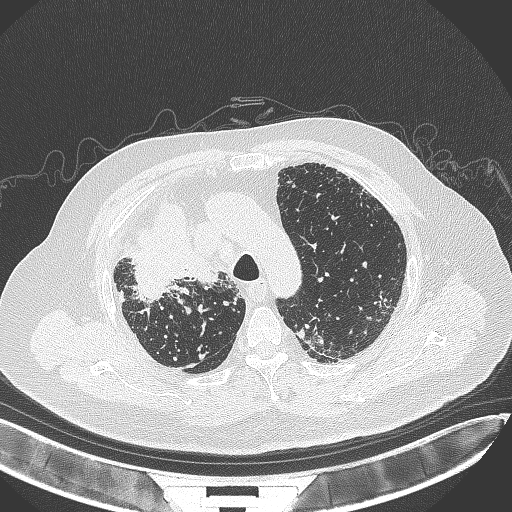
Chest CT, one axial slice. Position 269 of 384 along the scan axis. Lung window (W 1500 / L -600 HU). 1 mm slice thickness. 512 × 512 image matrix, field of view 400 × 400 mm. Male patient, age 69 years. From the clinical record (not read from this slice): clinical TNM (as recorded): T4 N3 M1.
Annotated regions visible in this slice (rectangle marked by the reading radiologist):
- lung tumour (recorded histology: adenocarcinoma): bounding box (x1, y1, x2, y2) in pixels: (123, 201, 227, 299)